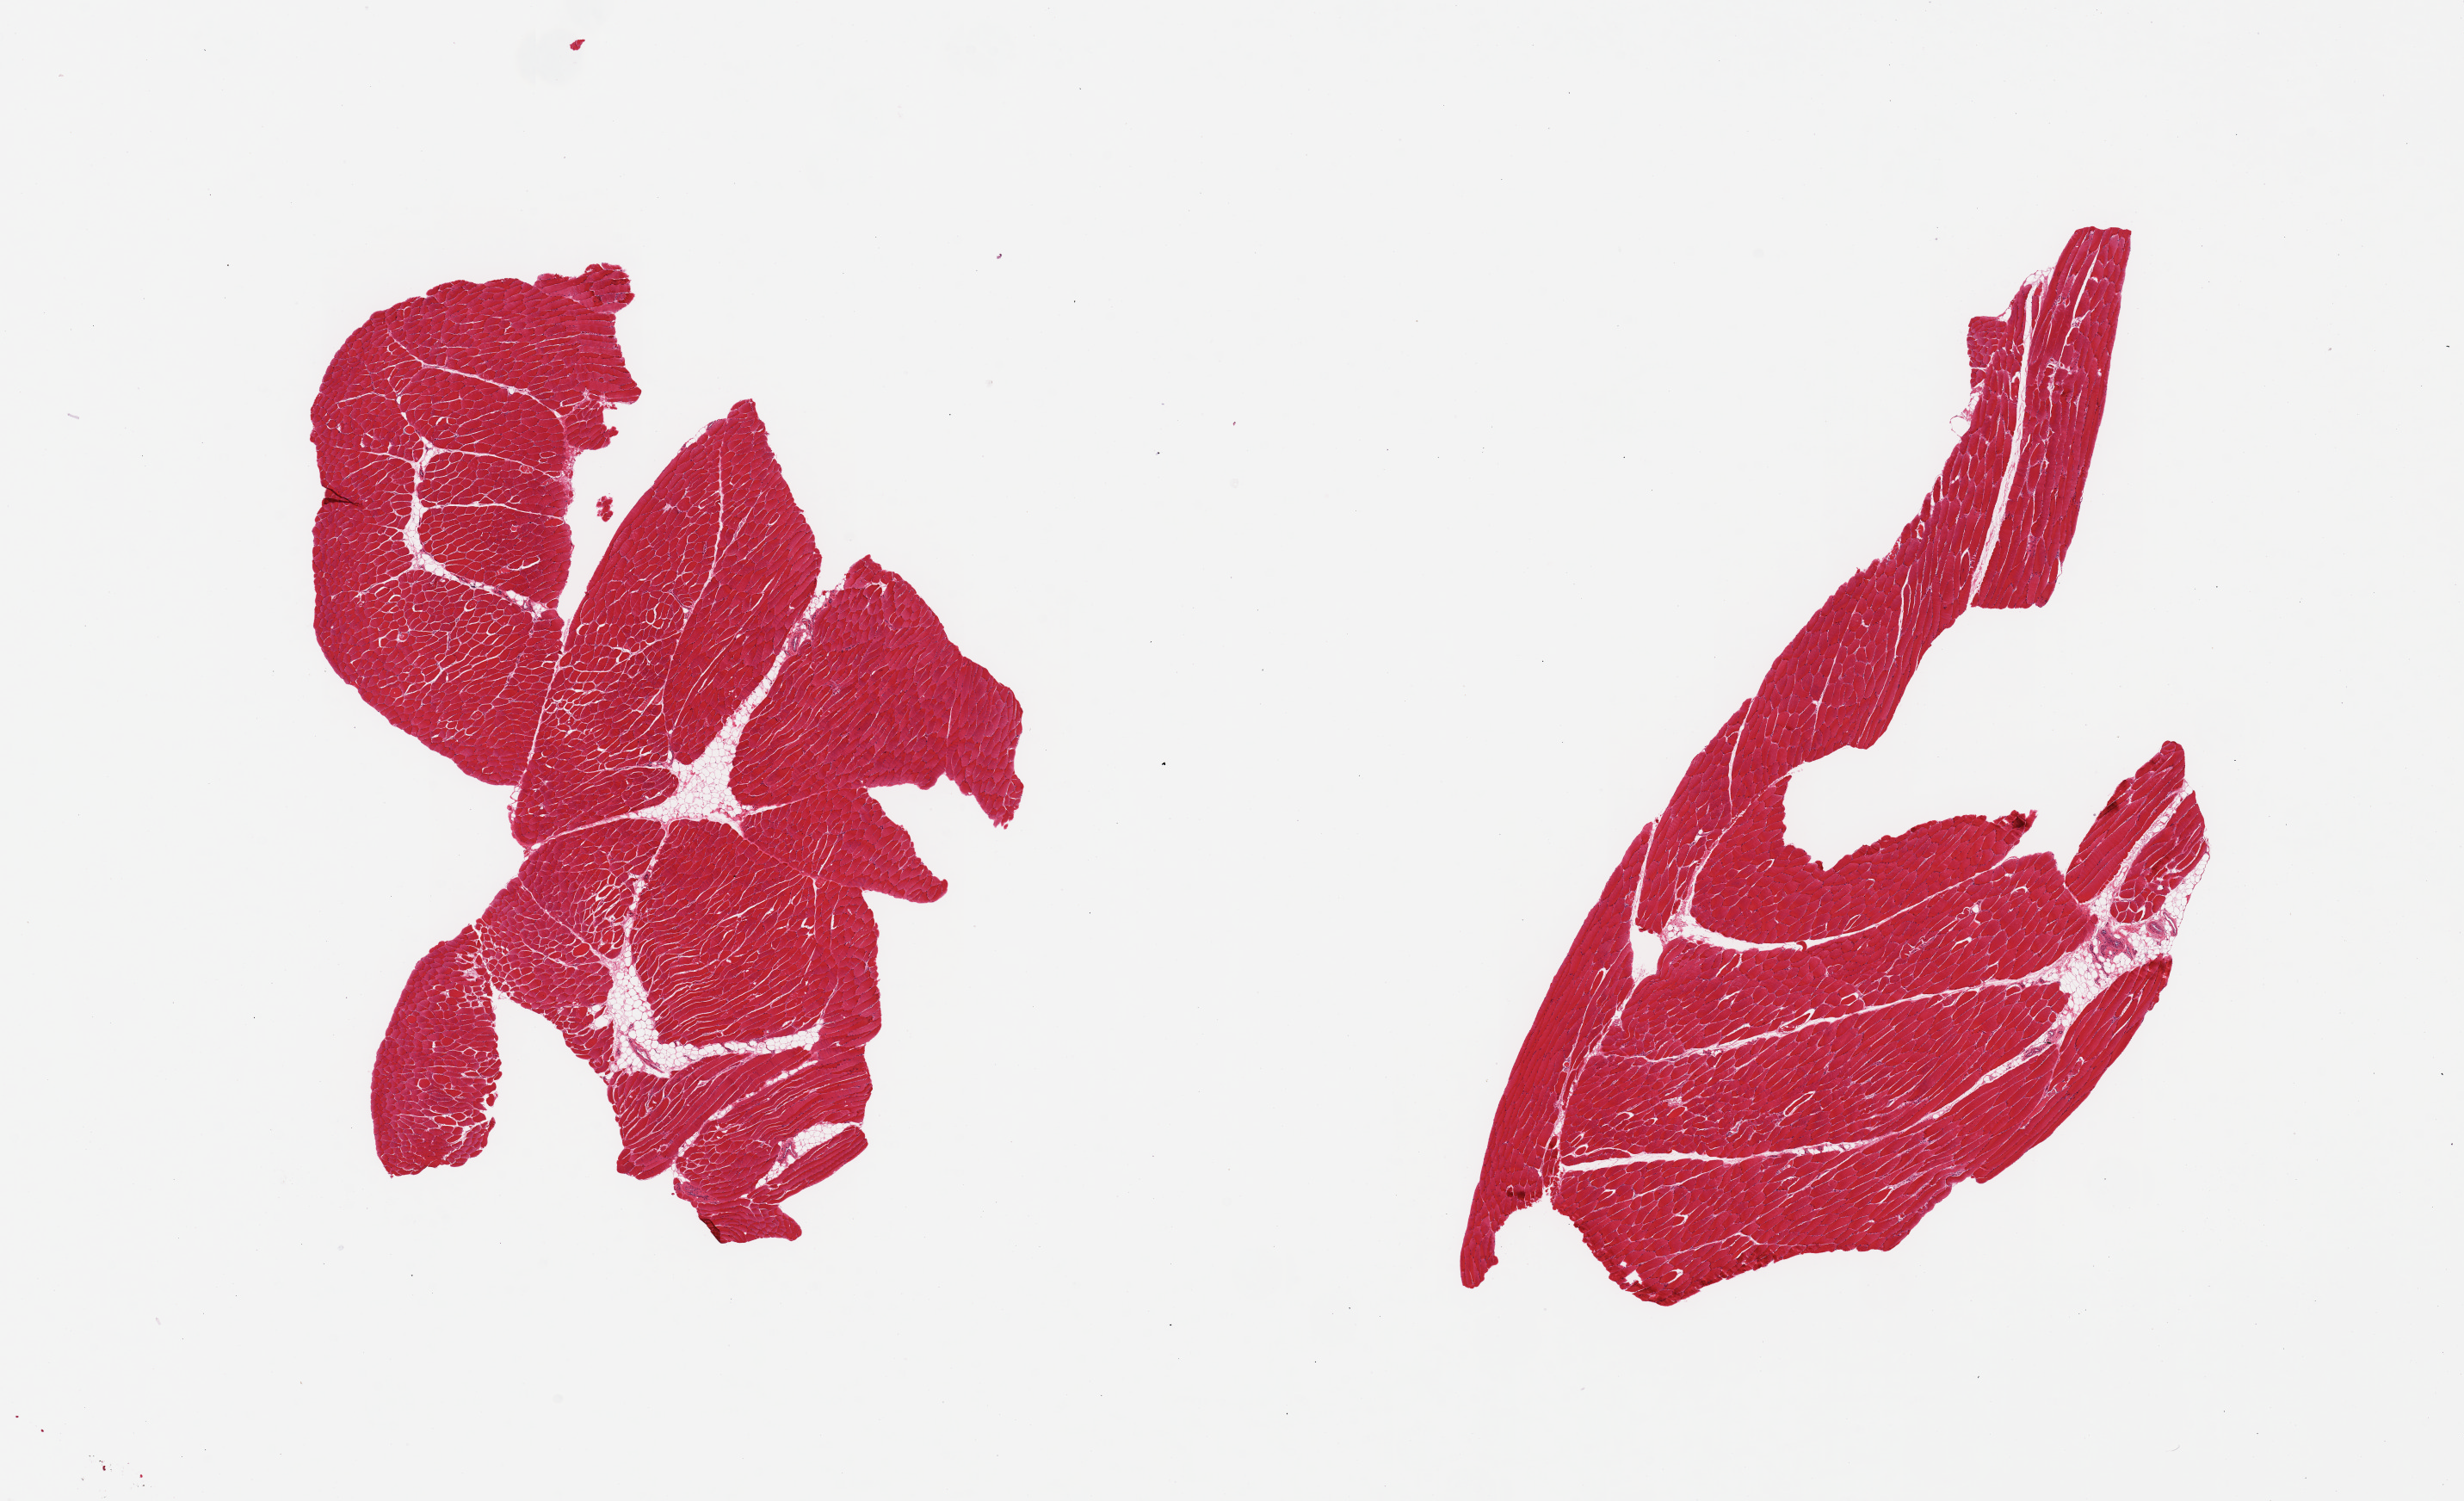
Whole-slide image, haematoxylin and eosin stain, whole scanned area (about 22.6 x 13.8 mm, acquisition: 20x scan) shown as a low-resolution overview. PAXgene-fixed paraffin-embedded (PFPE) section. Section of skeletal muscle (target tissue). Donor tissue sample. Donor sex: female.
Pathologist's review note for this sample: 2 pieces, interstitial fat/fvascular elements ~5-10% of tissue.